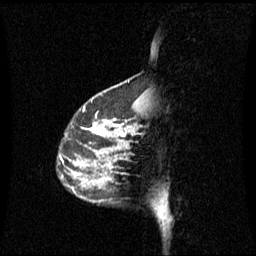
Breast MRI (dynamic contrast-enhanced), one sagittal slice. Slice 18 of 60 in the series (ordered by position). Dynamic contrast-enhanced series, image 2 of 3 at this slice position (ordered by acquisition). 1.5 T. TE 4.2 ms, TR 8.4 ms. 2.1 mm slice thickness. 256 × 256 image matrix. Female patient, age 42 years. From the clinical record (not read from this slice): setting: breast cancer imaged before/during neoadjuvant chemotherapy; receptor status: HR-positive, HER2-negative.
Structures marked on this image (semi-automatically segmented with operator editing):
- analysis volume of interest (the breast-tissue region the enhancement analysis was run in; not a lesion): box from (x=70, y=100) to (x=137, y=189) px
- tumour enhancement mask (voxels above the 70 % enhancement threshold inside the analysis volume of interest): (x=84, y=120)–(x=127, y=137)